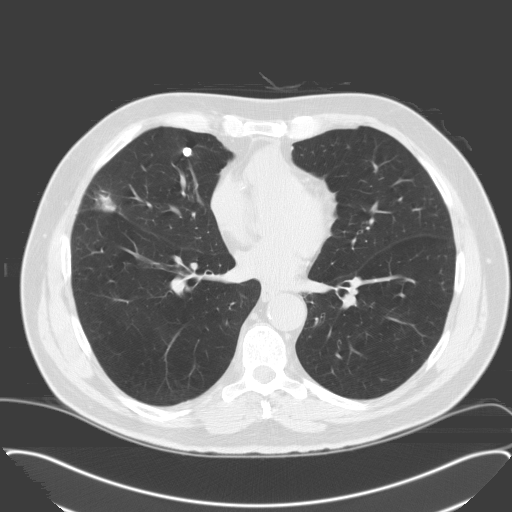
Low-dose screening chest CT, one axial slice; position 83 of 174 along the scan axis; 120 kVp; lung window (W 1500 / L -600 HU); 512 × 512 image matrix, field of view 400 × 400 mm.
Annotated regions visible in this slice (expert manual segmentation):
- lesion 1 (tumor, middle lobe of right lung): bounding box (x1, y1, x2, y2) in pixels: (91, 192, 117, 212)